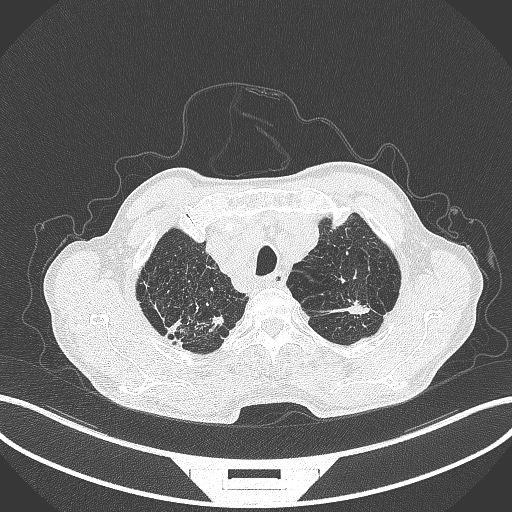
Chest CT, one axial slice; slice 387 of 463 in the series (ordered by position); lung window (W 1500 / L -600 HU); 1 mm slice thickness; 512 × 512 image matrix. Male patient, age 74 years. From the clinical record (not read from this slice): clinical TNM (as recorded): T2a N1 M0.
Annotated regions visible in this slice (rectangle marked by the reading radiologist):
- lung tumour (recorded histology: adenocarcinoma): bounding box [x1, y1, x2, y2] px = [330, 295, 378, 317]